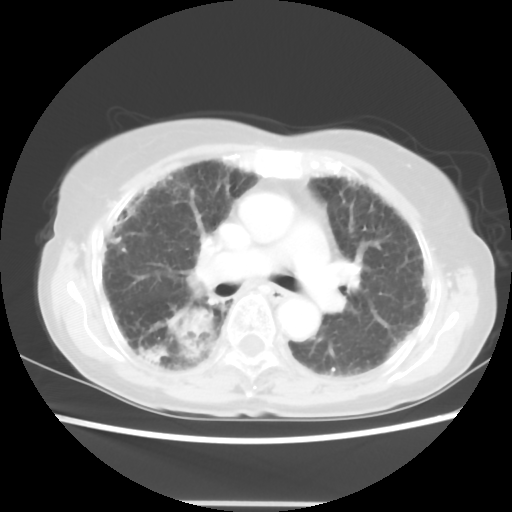
Chest CT, one axial slice; position 32 of 52 along the scan axis; 120 kVp; lung window (W 1500 / L -600 HU); 5 mm slice thickness; 512 × 512 image matrix, field of view 325 × 325 mm. Patient: female, 71 years. Case-level facts recorded for this patient, not image findings: clinical TNM (as recorded): T3 N0 M0.
Outlined on this slice (rectangle marked by the reading radiologist):
- lung tumour (recorded histology: squamous cell carcinoma): bounding box <164,303,219,362> (left, top, right, bottom; pixels)